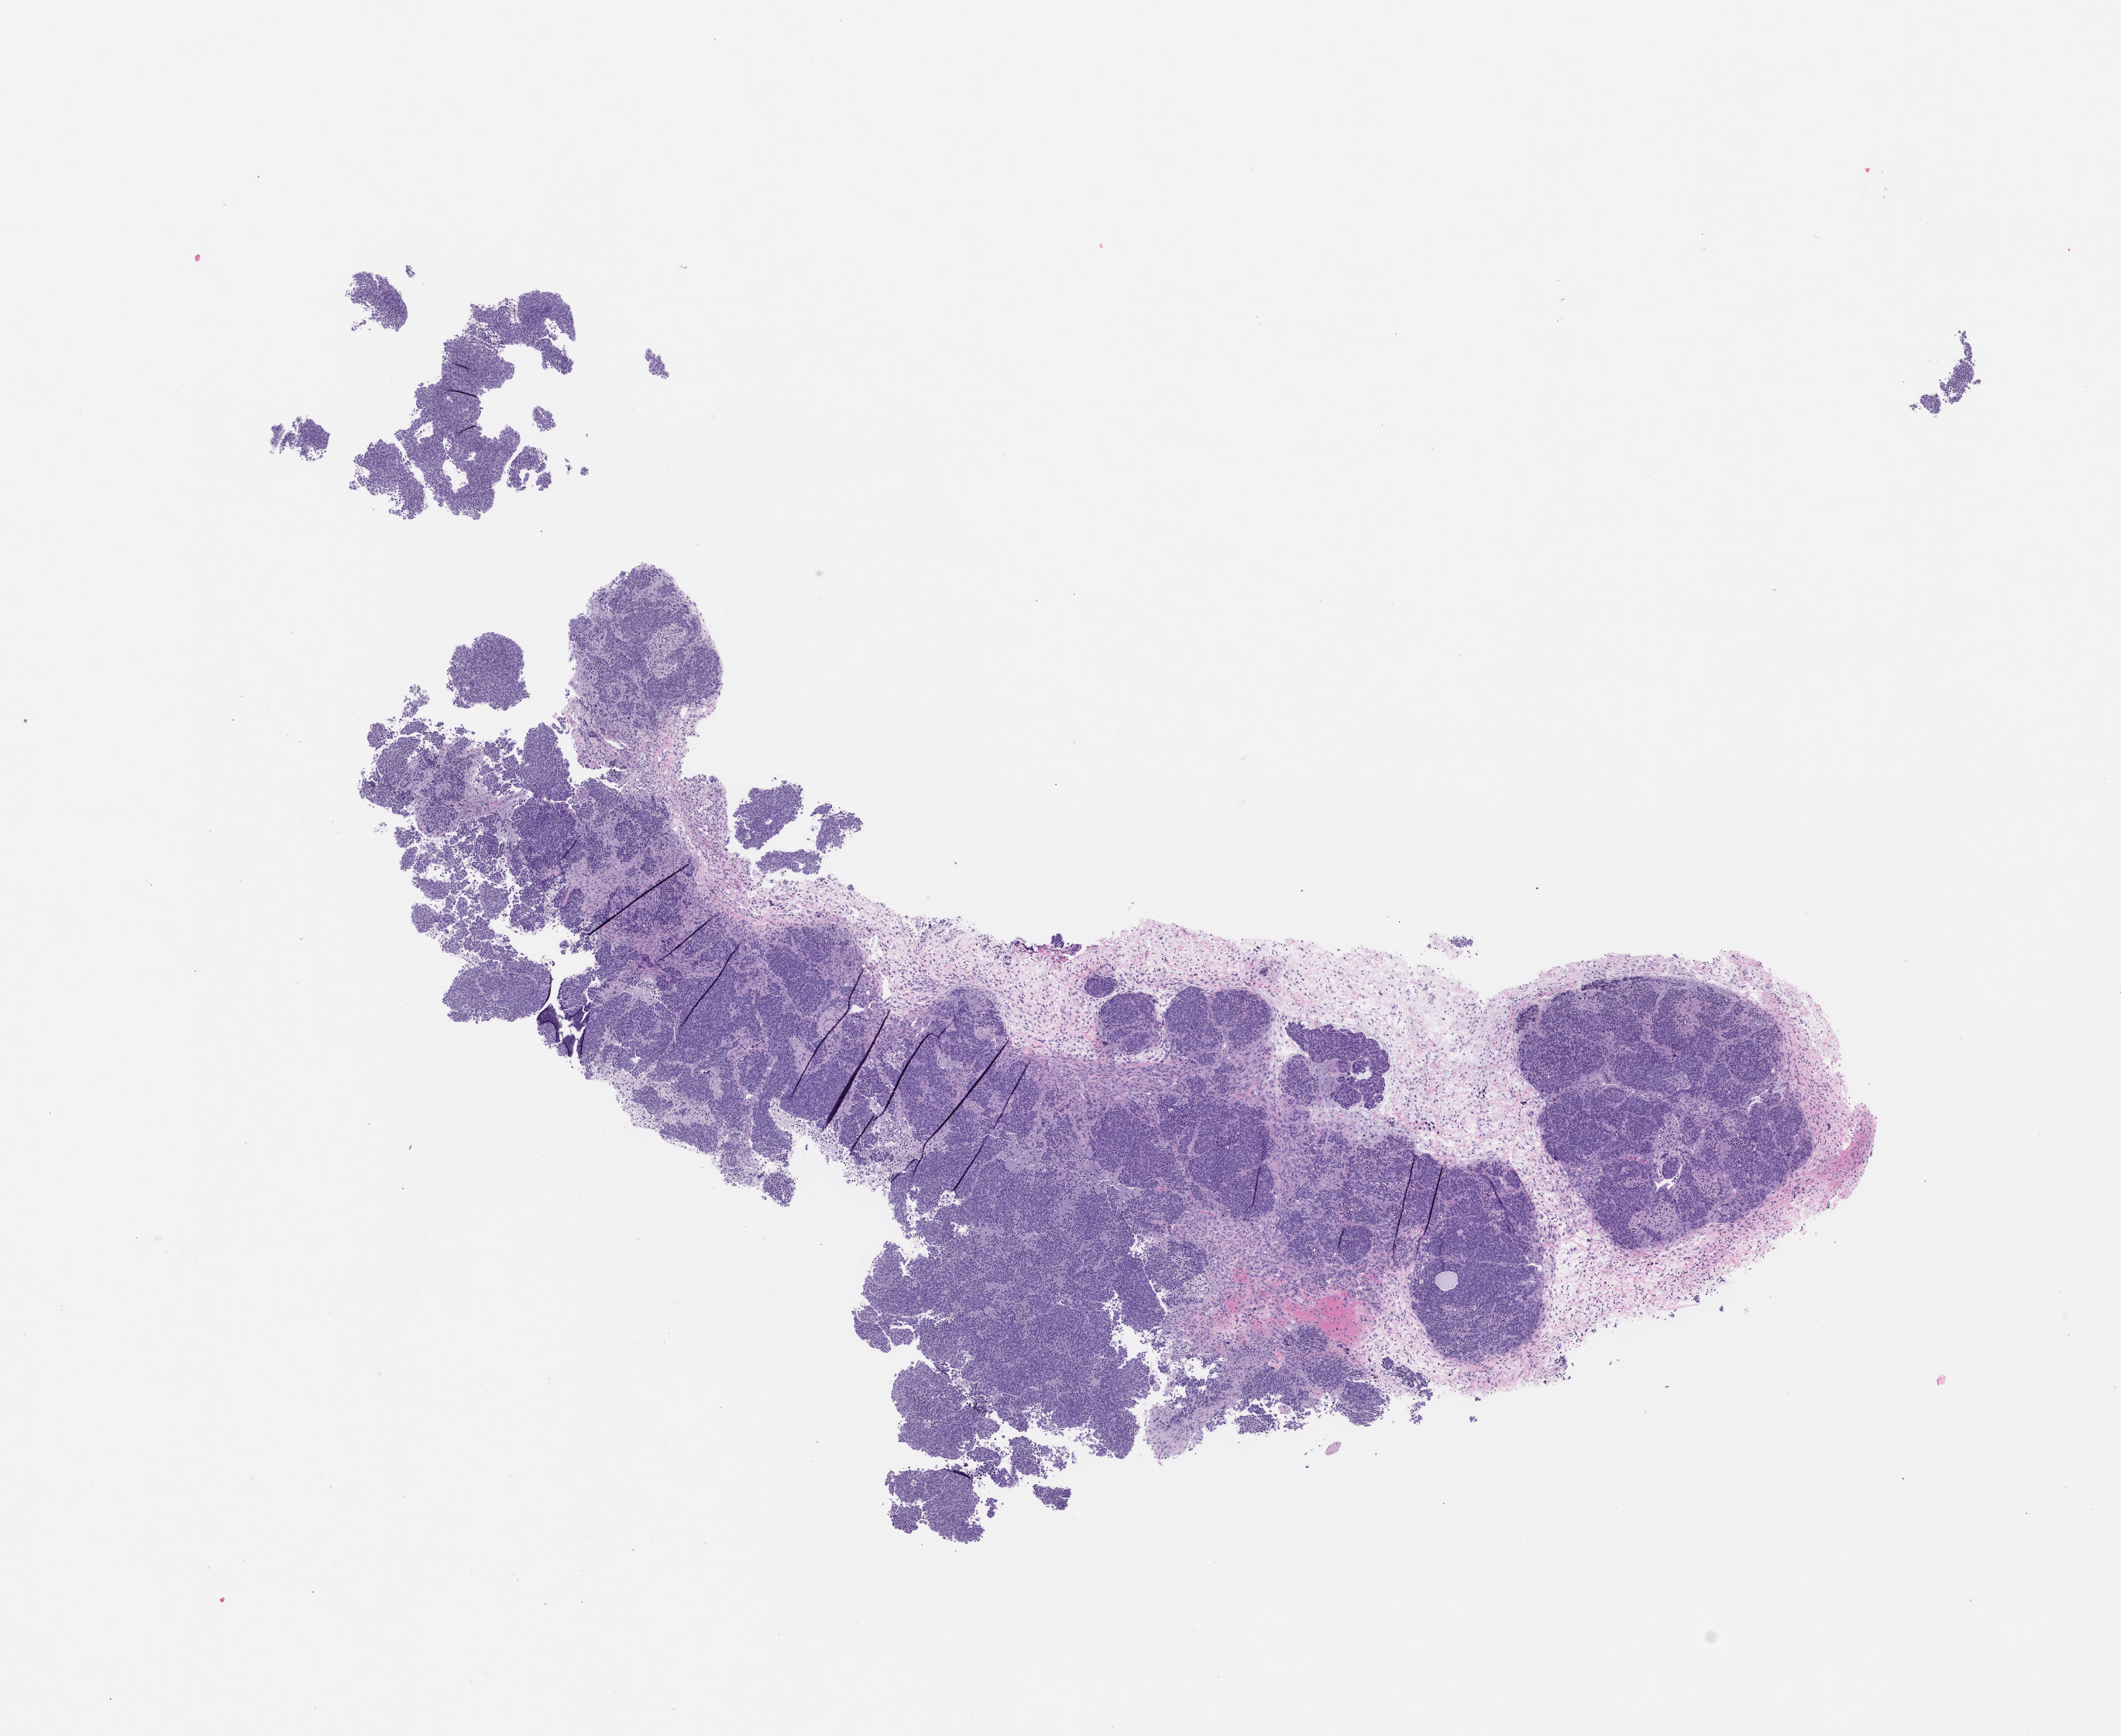
Whole-slide image, haematoxylin and eosin: patient-derived xenograft (human tumor grown in a mouse) — shown as a low-resolution overview of the whole scanned area (about 11.0 x 9.0 mm). Formalin-fixed, paraffin-embedded (FFPE) tissue. Originating tumor site category: lung.
Originating patient diagnosis: Lung Adenocarcinoma.